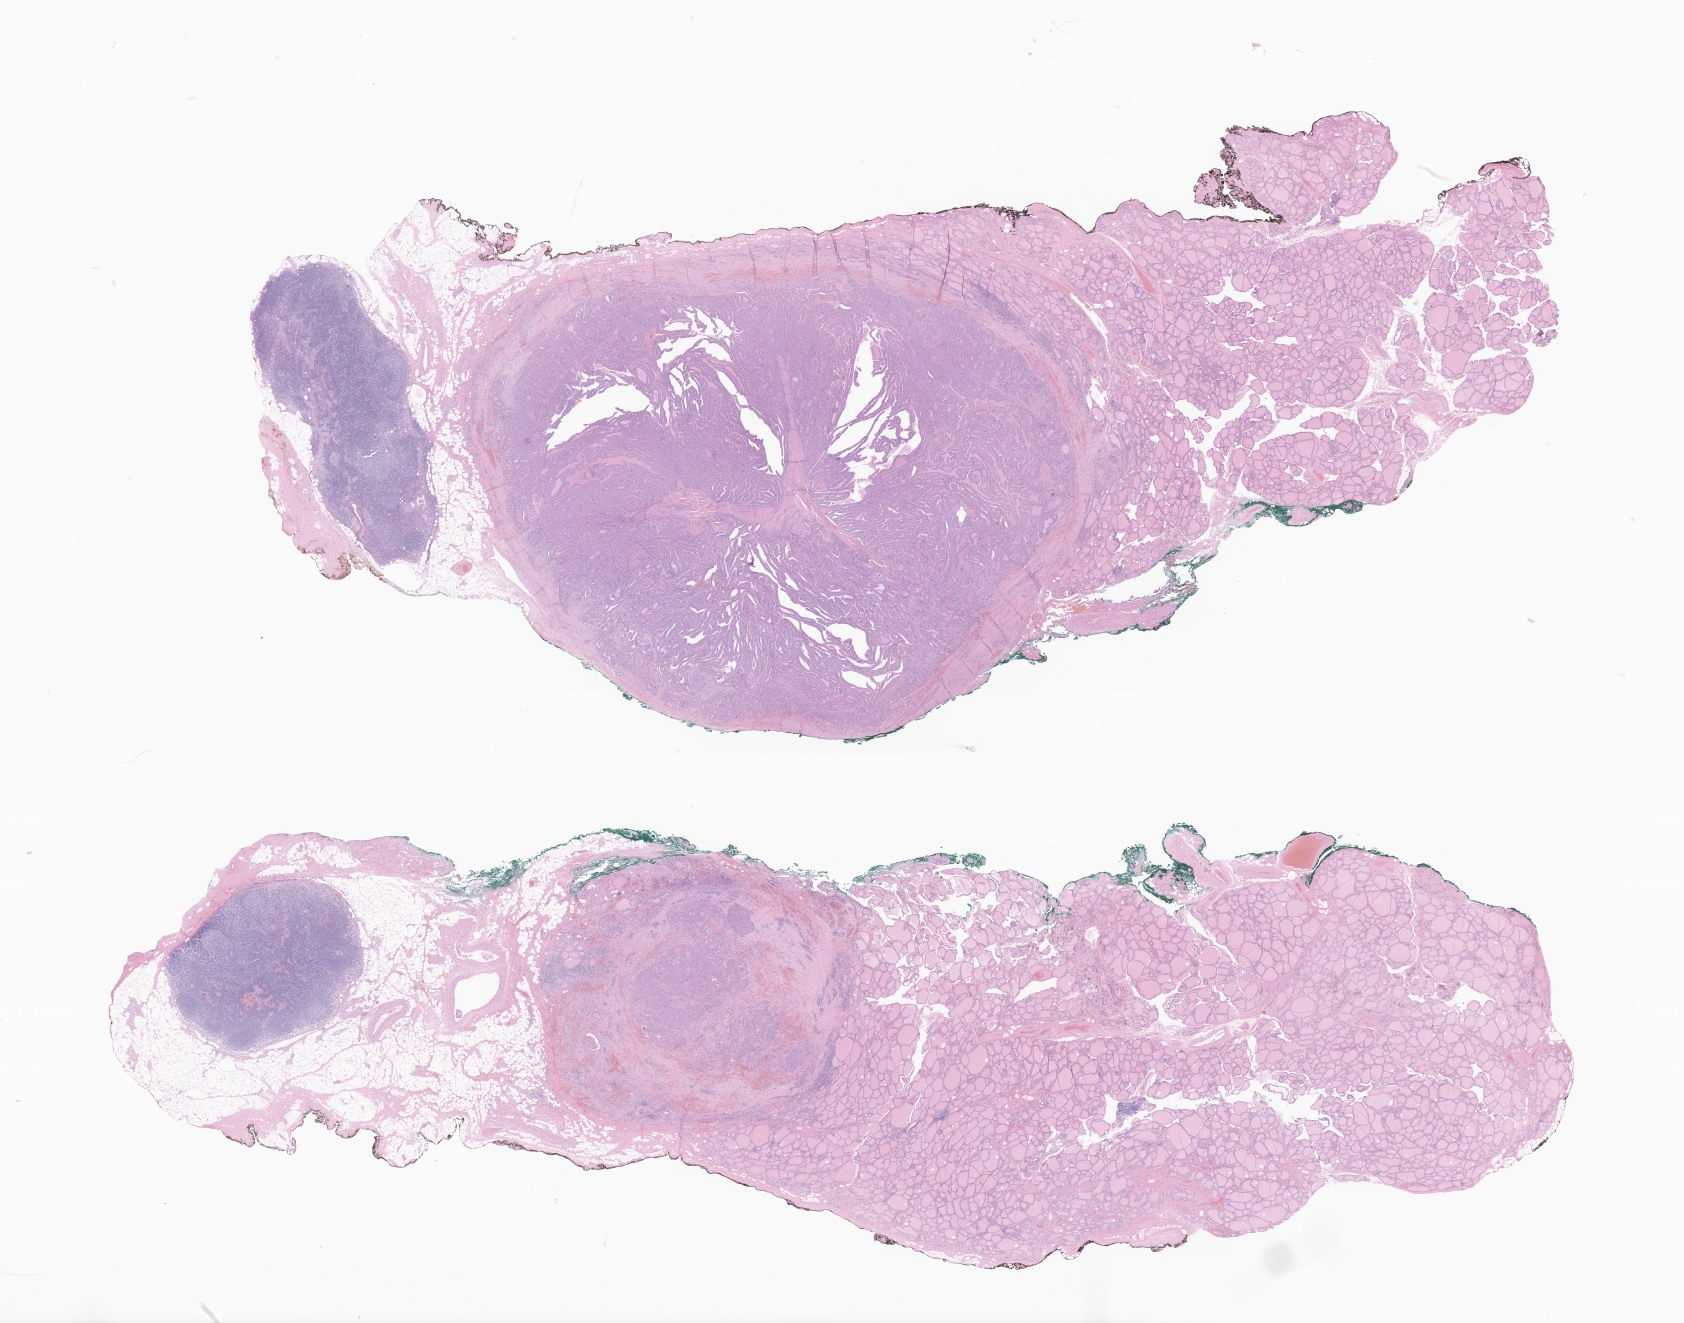
H&E whole-slide image of tumor tissue from the thyroid — shown as a low-resolution overview of the whole scanned area (about 28.4 x 22.3 mm); formalin-fixed, paraffin-embedded (FFPE) tissue. Patient male; age 184 months.
Diagnosis (ICD-O-3 morphology term): Papillary carcinoma, NOS.